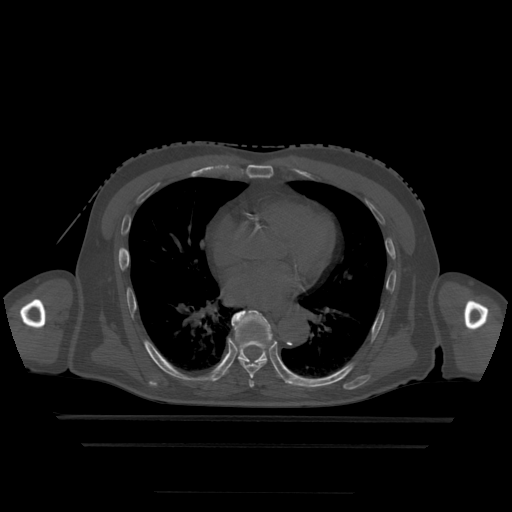
CT including the spine, one axial slice. Slice 291 of 522 in the series (ordered by position). Bone window (W 1800 / L 400 HU). 512 × 512 image matrix. Patient age 68 years. From the clinical record (not read from this slice): primary cancer: urothelial.
Structures marked on this image (semi-automatic segmentation, software-assisted and operator-edited):
- T6 vertebra: bounding box <249,380,255,388> (left, top, right, bottom; pixels)
- T7 vertebra: <241,362,267,379>
- T8 vertebra: <225,310,283,379>